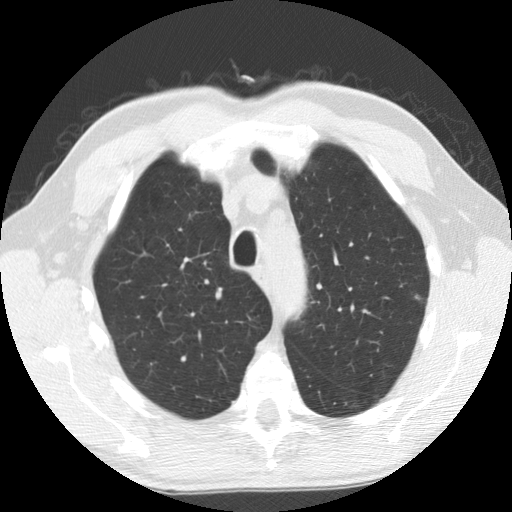
Chest CT (low-dose screening protocol), one axial image, third screening round (two years after baseline), lung window (W 1500 / L -600 HU), slice 31 of 158 in the series, 512 × 512 image matrix. Male, age 63 years at enrolment. Current smoker at enrolment.
Lesion marked by an expert reader, bounding box [x1, y1, x2, y2] px = [401, 283, 442, 317]. Screening reader's record for this exam (one nodule recorded; not confirmed to be the boxed lesion): non-calcified nodule or mass ≥4 mm, left upper lobe, 8 × 6 mm, smooth margins, ground glass attenuation, pre-existing on the prior screen: yes; interval growth: yes. Official screen result: positive, other. Participant outcome: lung cancer diagnosed 52 days after this screen — adenocarcinoma, NOS, left upper lobe, well differentiated (G1), stage IB (AJCC 6th edition), 5 mm at pathology.